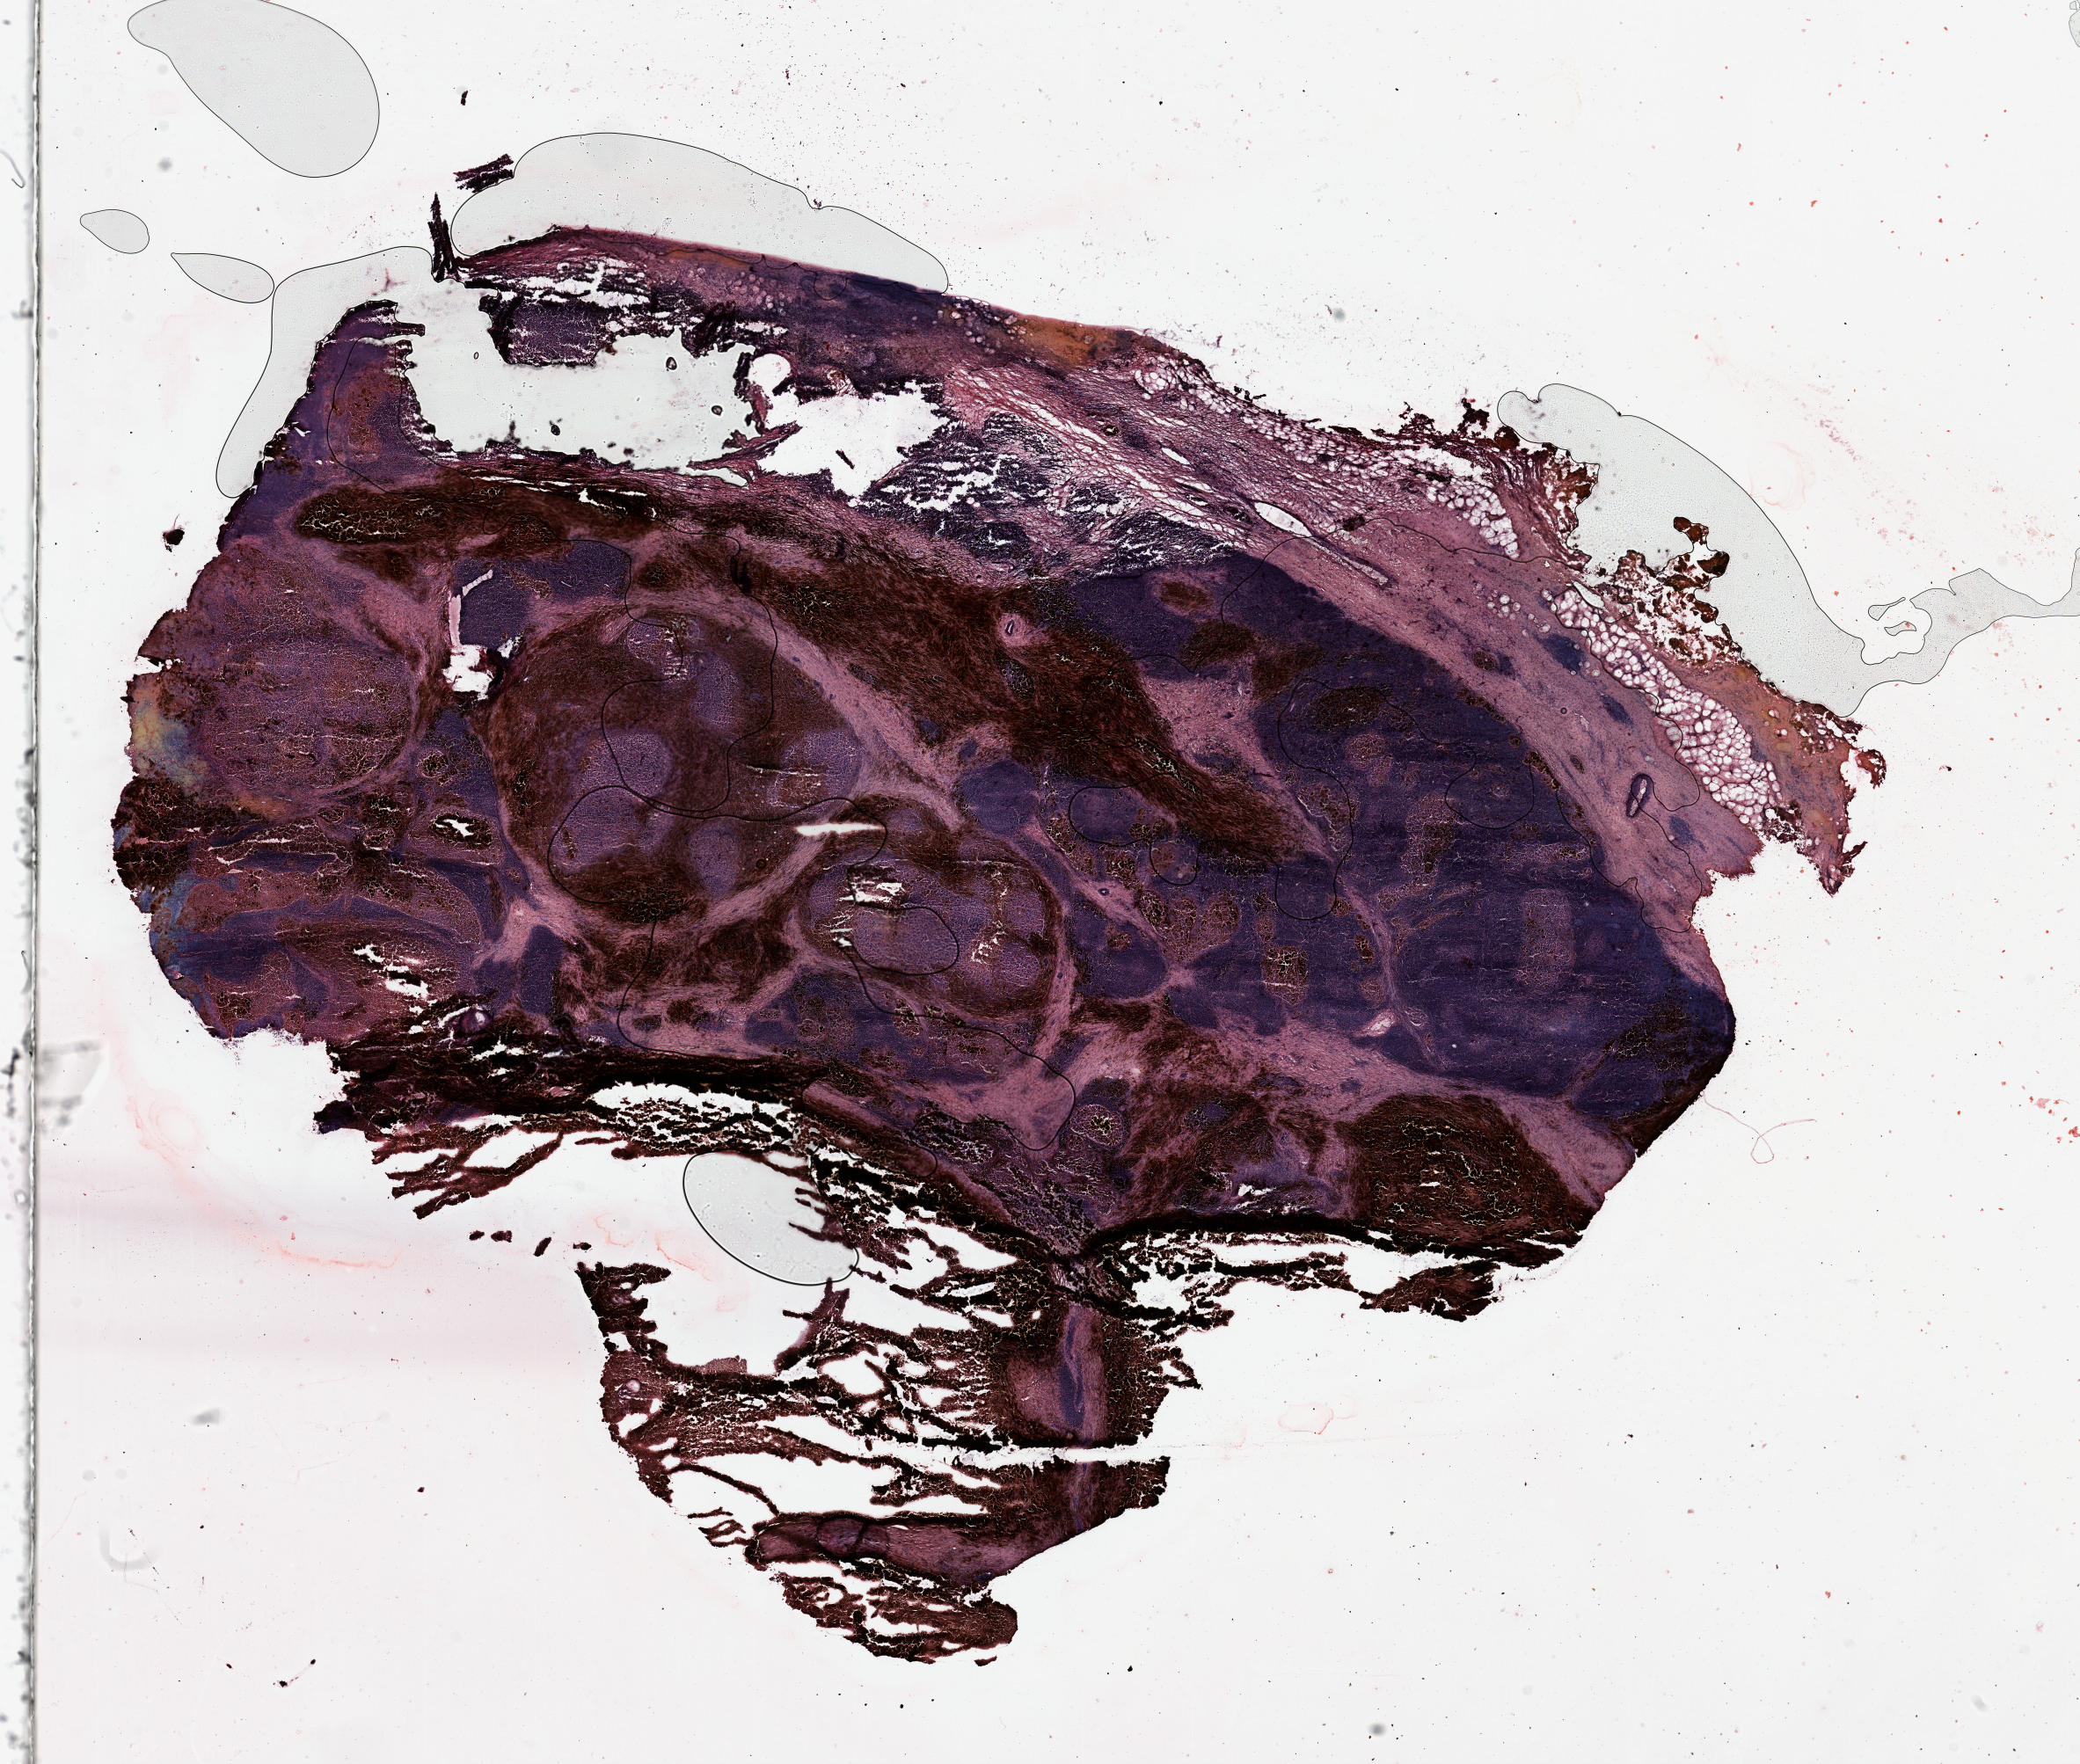
Digitized H&E-stained tissue section (whole slide), low-resolution overview of the scanned area, about 18.7 x 15.9 mm (slide scanned at 20x). Melanoma tumour tissue; sampled site not recorded. Patient: female, age 23 years.
* patient diagnosis (cohort enrolment): cutaneous melanoma (skin)